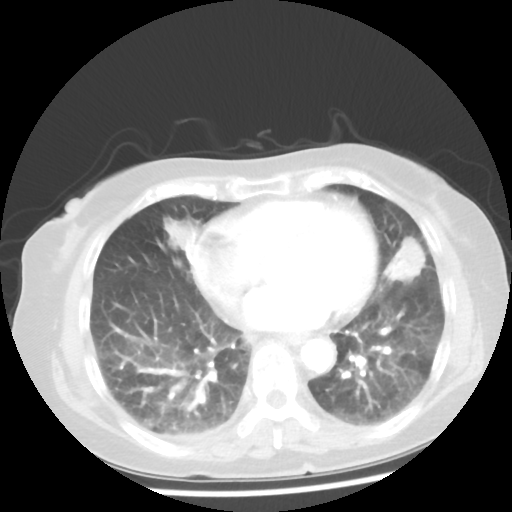
Chest CT, one axial slice. Position 18 of 50 along the scan axis. Reconstruction kernel STANDARD. 100 kVp. Lung window (W 1500 / L -600 HU). 512 × 512 image matrix, field of view 332 × 332 mm. Patient: female, 77 years. From the clinical record (not read from this slice): clinical TNM (as recorded): T2 N3 M1a.
Outlined on this slice (rectangle marked by the reading radiologist):
- lung tumour (recorded histology: adenocarcinoma): box from (x=382, y=229) to (x=430, y=291) px